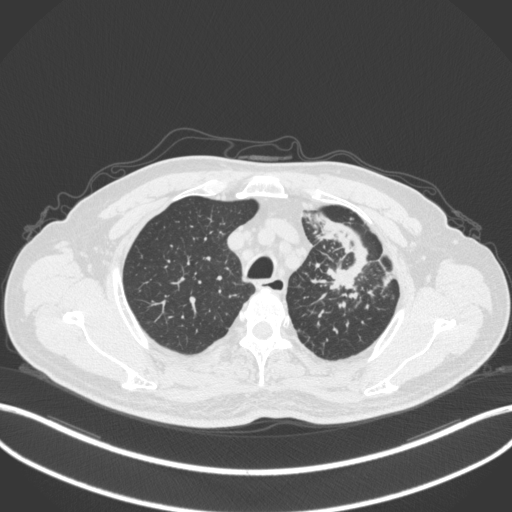
Chest CT, one axial slice; slice 290 of 386 in the series (ordered by position); lung window (W 1500 / L -600 HU); 512 × 512 image matrix, field of view 400 × 400 mm. Patient: male, 69 years. From the clinical record (not read from this slice): clinical TNM (as recorded): T2a N2 M0.
Outlined on this slice (bounding box drawn by a radiologist):
- lung tumour (recorded histology: adenocarcinoma): bounding box <311,214,370,298> (left, top, right, bottom; pixels)